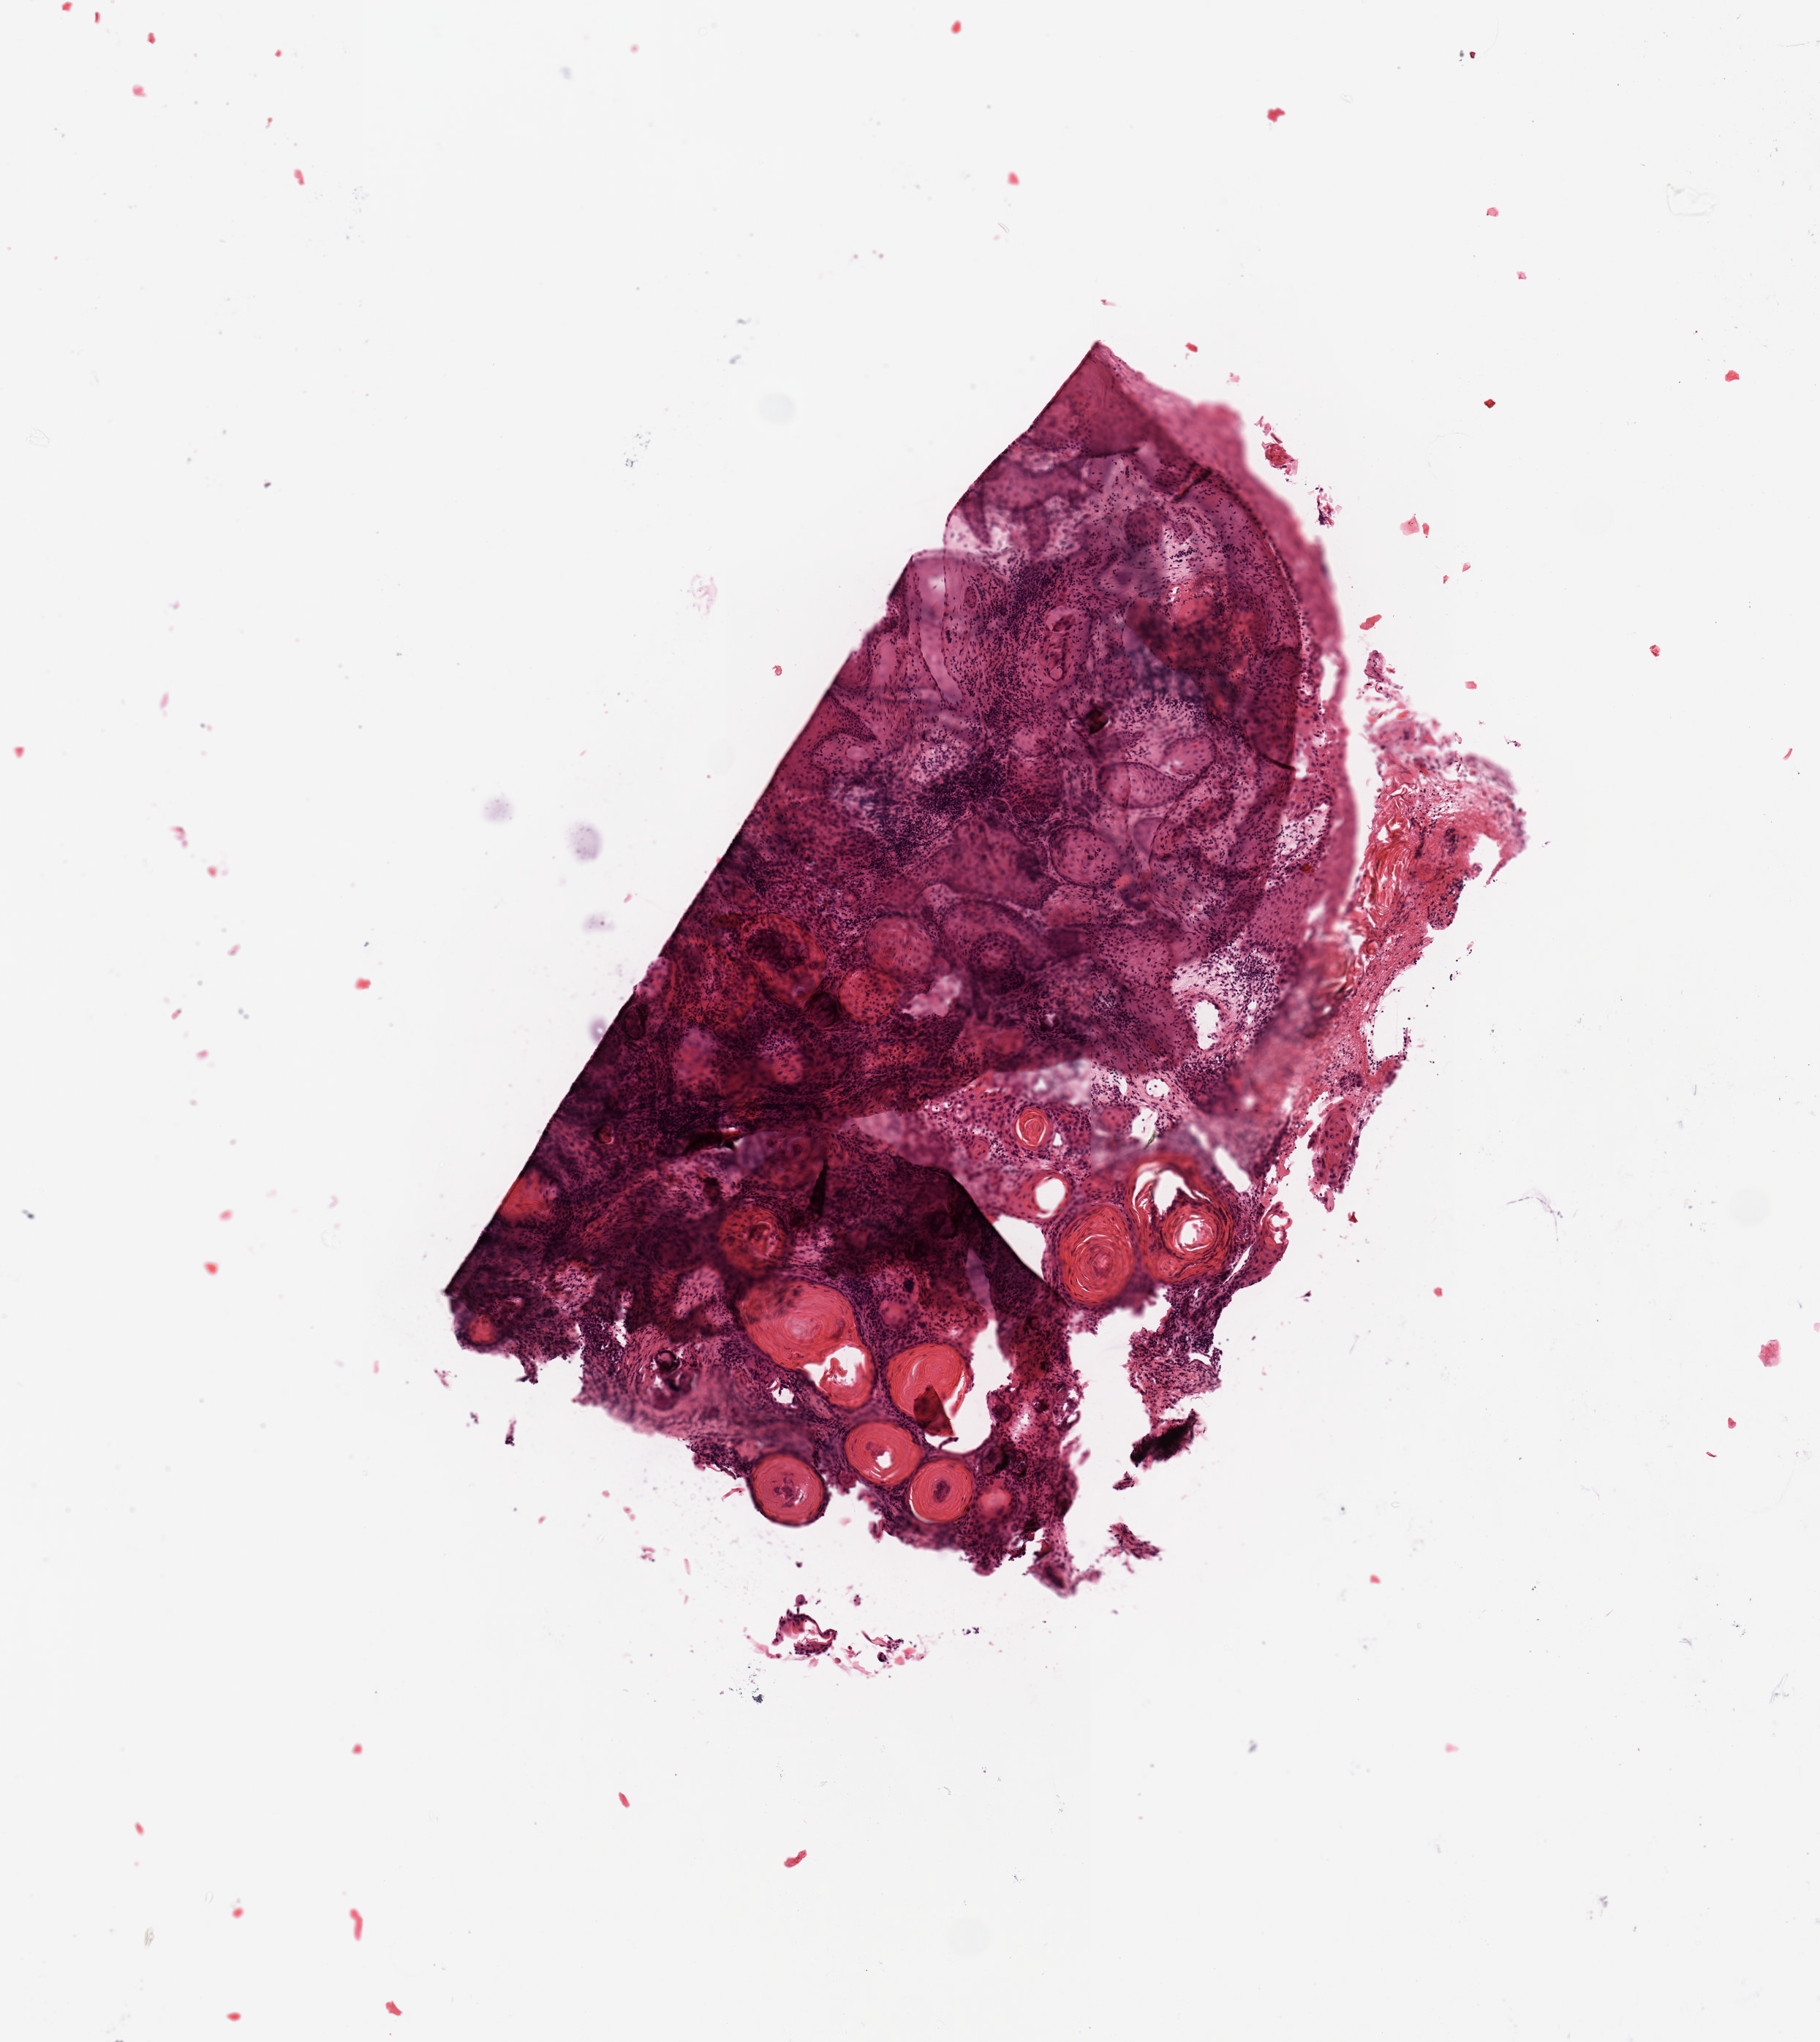
H&E whole-slide image, a low-resolution overview of the entire scanned area, about 4.9 x 5.5 mm. Tumour tissue sample, sampled site: floor of mouth. Male, 59 y/o. Histologic grade: G2 (moderately differentiated). Composition of this section per pathologist review: tumour nuclei 85%, necrosis 3%.
- histologic diagnosis: Squamous cell carcinoma, NOS (floor of mouth, NOS)
- AJCC pathologic stage: IVA
- primary tumour site (as recorded): oral cavity